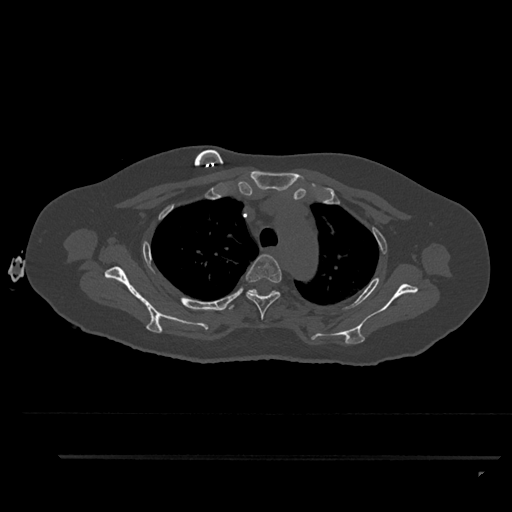
CT including the spine, one axial slice; slice 675 of 797 in the series (ordered by position); reconstruction kernel Br40s/3; bone window (W 1800 / L 400 HU); 0.5 mm slice thickness; 512 × 512 image matrix, field of view 408 × 408 mm. Patient: female, 44 years. Case-level facts recorded for this patient, not image findings: primary cancer: renal.
Structures marked on this image (semi-automatic segmentation, software-assisted and operator-edited):
- T3 vertebra: bounding box (x1, y1, x2, y2) in pixels: (246, 254, 282, 320)
- T4 vertebra: (229, 289, 280, 310)